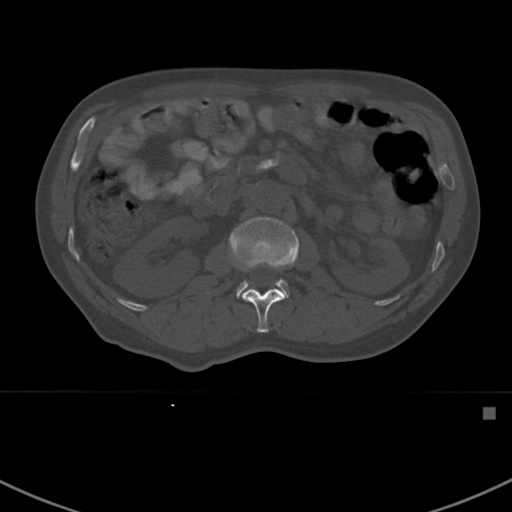
CT including the spine, one axial slice; position 299 of 412 along the scan axis; 120 kVp; bone window (W 1800 / L 400 HU); 1.5 mm slice thickness; 512 × 512 image matrix. Male patient, age 59 years. From the clinical record (not read from this slice): primary cancer: prostate.
Structures marked on this image (semi-automatic segmentation, software-assisted and operator-edited):
- L1 vertebra: box from (x=242, y=288) to (x=285, y=333) px
- L2 vertebra: (x=228, y=216)–(x=299, y=299)